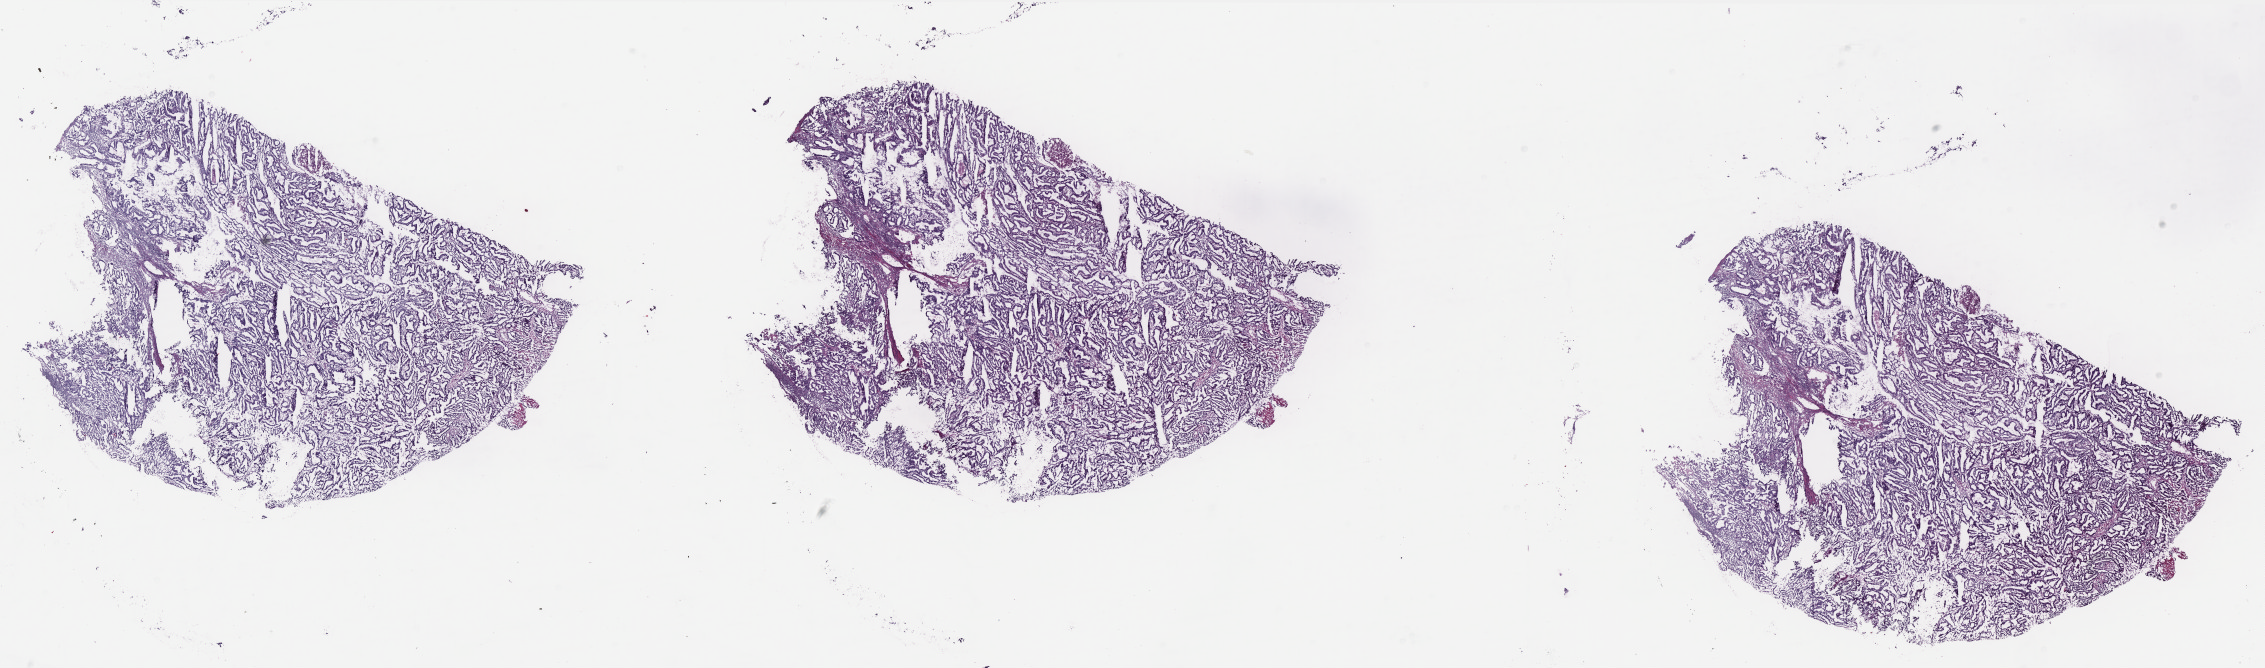
Digitized Hematoxylin and eosin (H&E) stained tissue section (whole slide), low-resolution overview of the scanned area, about 36.3 x 10.7 mm, frozen section from the bottom of the tissue portion, uterus, primary tumour sample. Female patient; age at initial diagnosis 53 years. Histologic grade: G1 (well differentiated). Composition of this section per pathologist review: tumour cells 95%, tumour nuclei 90%, normal cells 5%, stromal cells 0%, necrosis 0%. Infiltration values recorded for this section: lymphocyte infiltration 1%, monocyte infiltration 0%, neutrophil infiltration 0%.
* histologic diagnosis: Endometrioid adenocarcinoma, NOS
* FIGO stage: IA